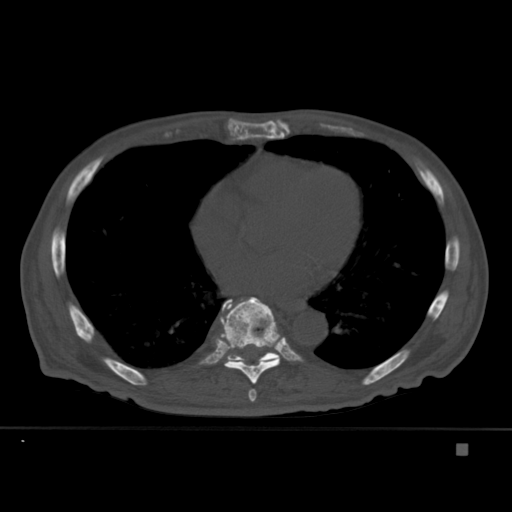
CT including the spine, one axial slice. Bone window (W 1800 / L 400 HU). 512 × 512 image matrix, field of view 378 × 378 mm. Male patient, age 75 years. From the clinical record (not read from this slice): primary cancer: prostate.
Annotated regions visible in this slice (semi-automatic segmentation, software-assisted and operator-edited):
- T7 vertebra: bounding box [x1, y1, x2, y2] px = [248, 389, 257, 402]
- T8 vertebra: [220, 297, 280, 384]
- T9 vertebra: [224, 325, 280, 367]